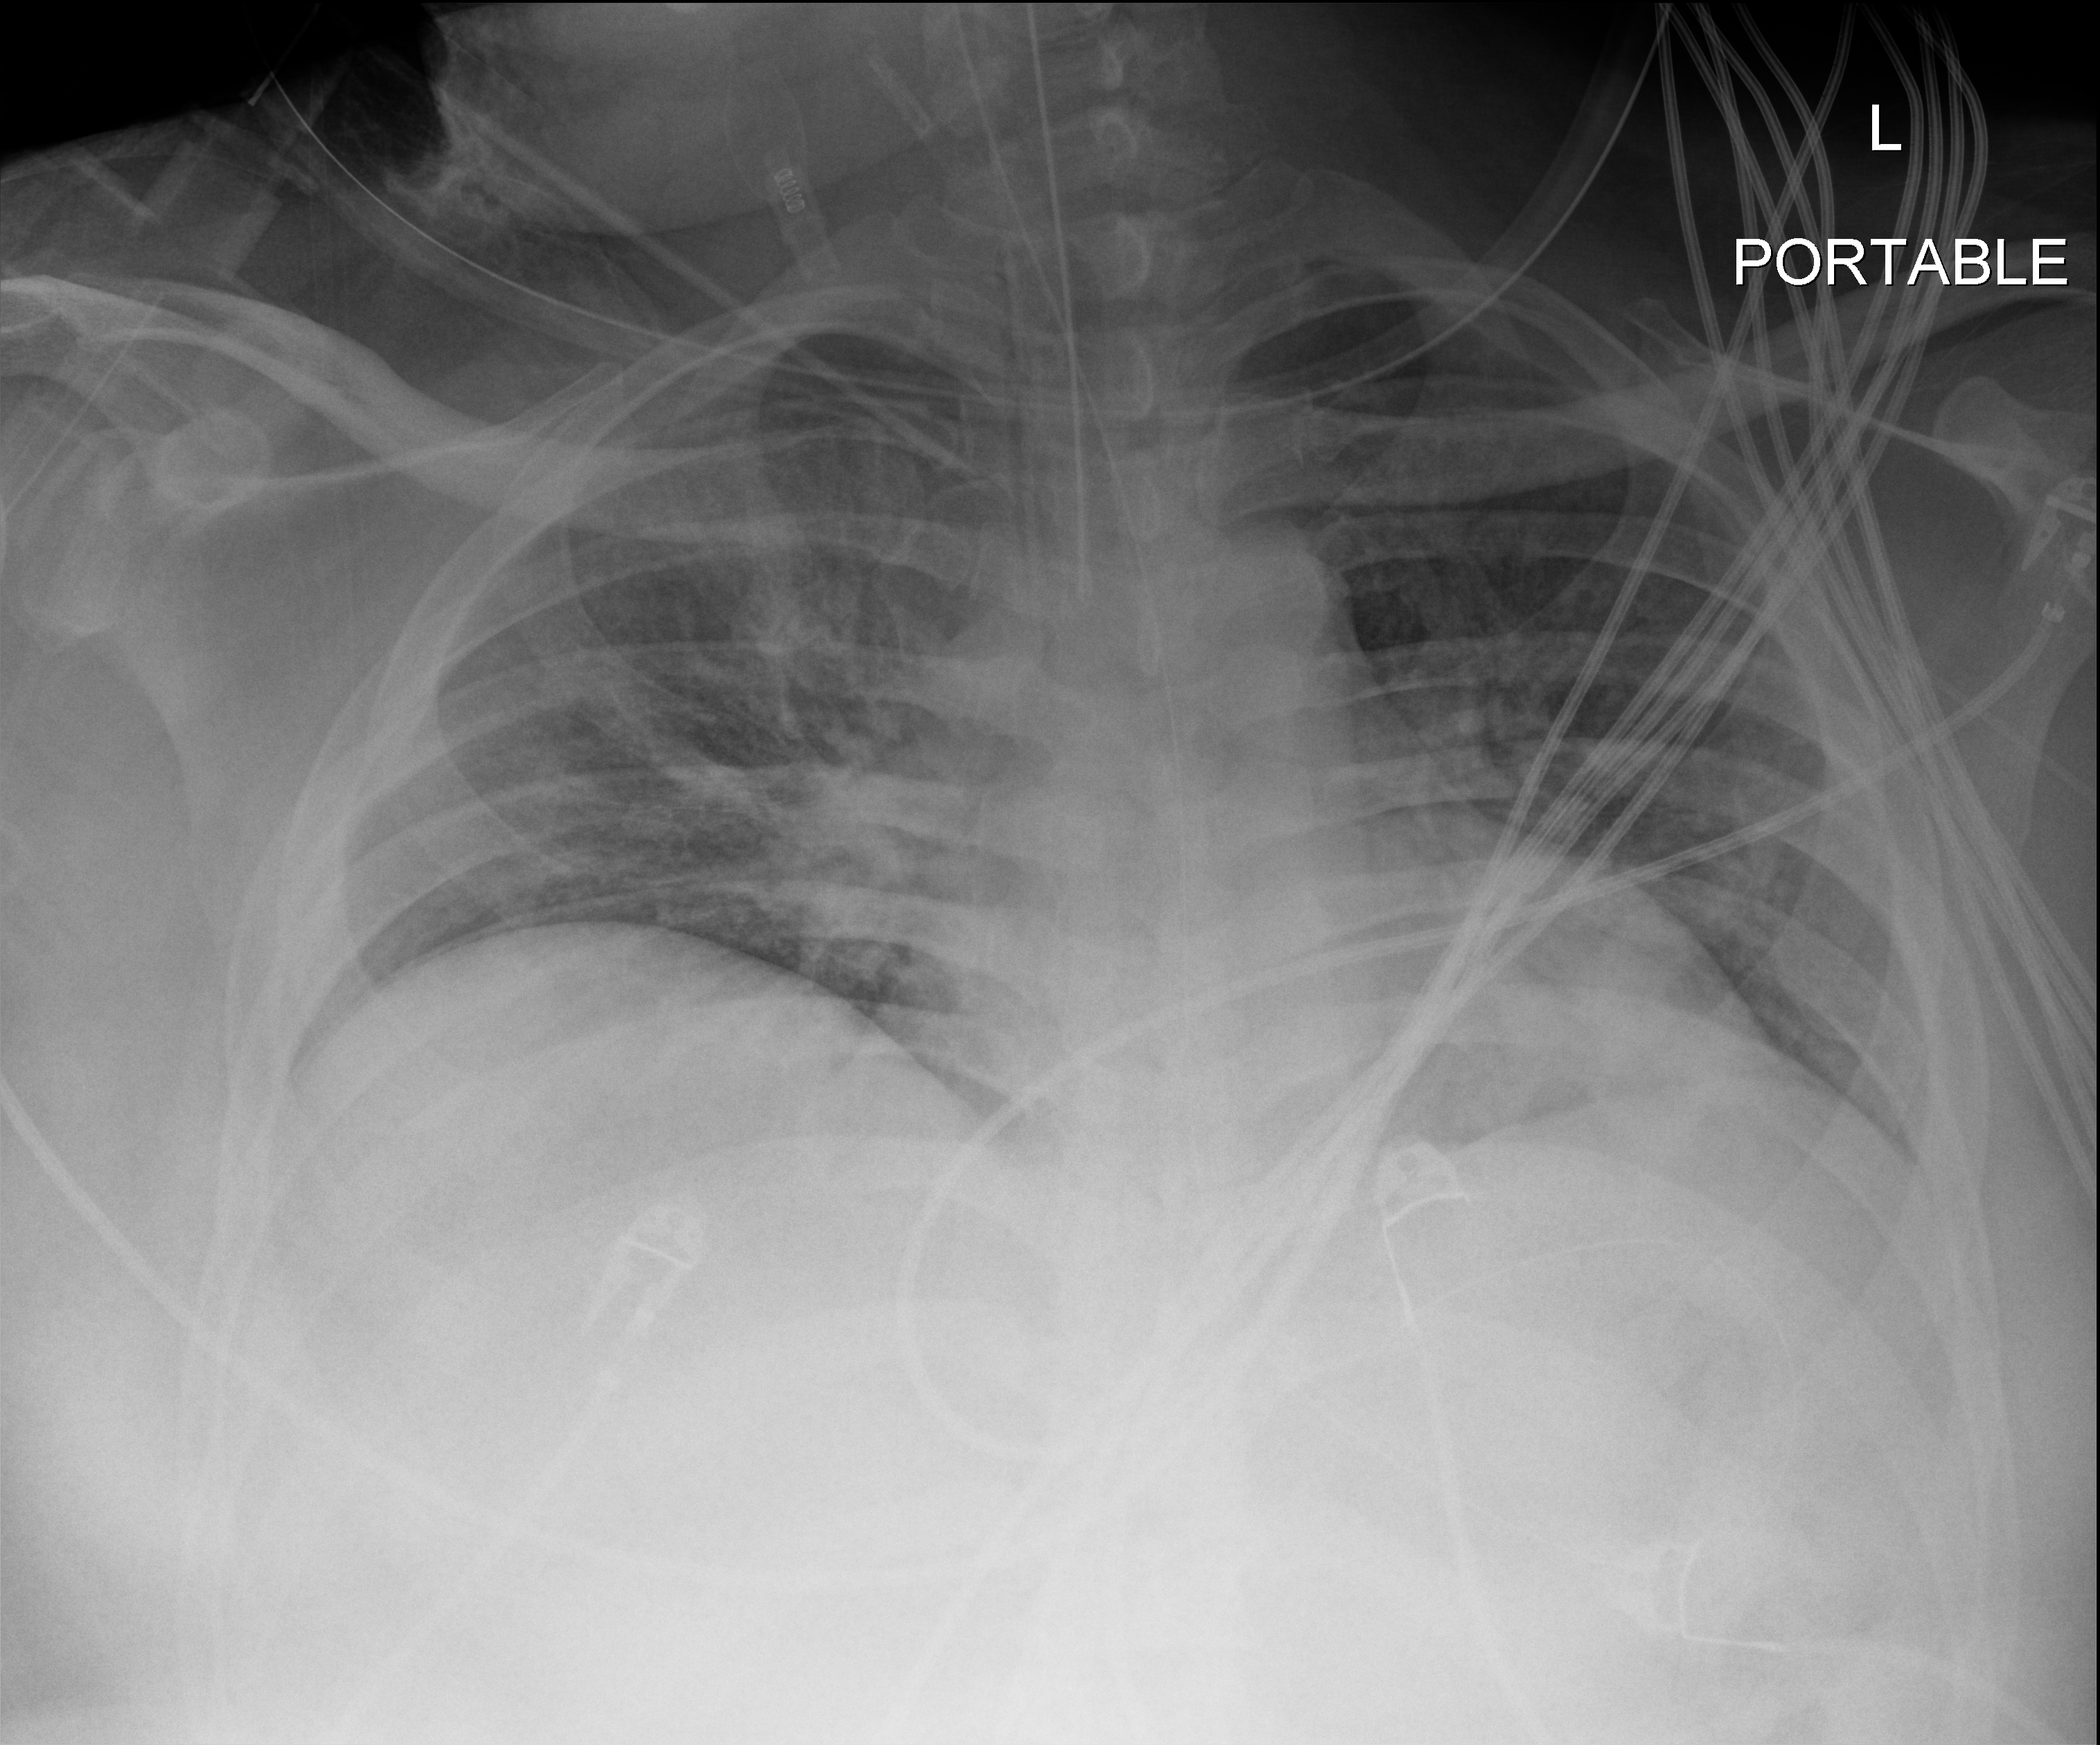
Portable chest radiograph. Patient hospitalised with COVID-19; male, aged 18–59 years.
From the hospital-stay record, not from the radiograph (when in the stay this image was taken is not recorded): admitted to intensive care during this hospital stay: yes; COPD (admission record): yes.